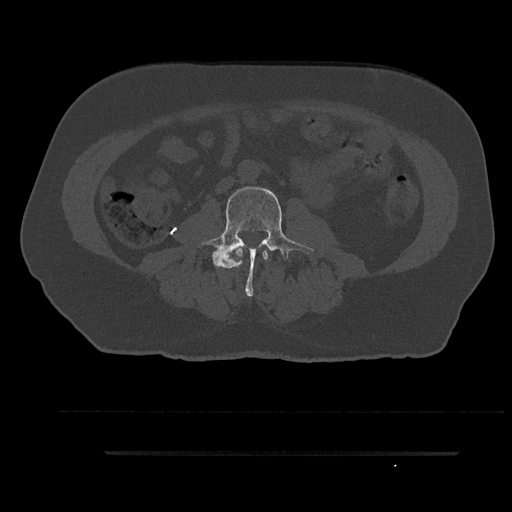
CT including the spine, one axial slice. Position 45 of 797 along the scan axis. Reconstruction kernel Br40s/3. 120 kVp. Bone window (W 1800 / L 400 HU). 0.5 mm slice thickness. 512 × 512 image matrix, field of view 432 × 432 mm. Patient: male, 63 years. Case-level facts recorded for this patient, not image findings: primary cancer: renal.
Structures marked on this image (semi-automatically segmented with operator editing):
- L2 vertebra: bounding box [x1, y1, x2, y2] px = [235, 248, 268, 267]
- L3 vertebra: [198, 185, 314, 296]